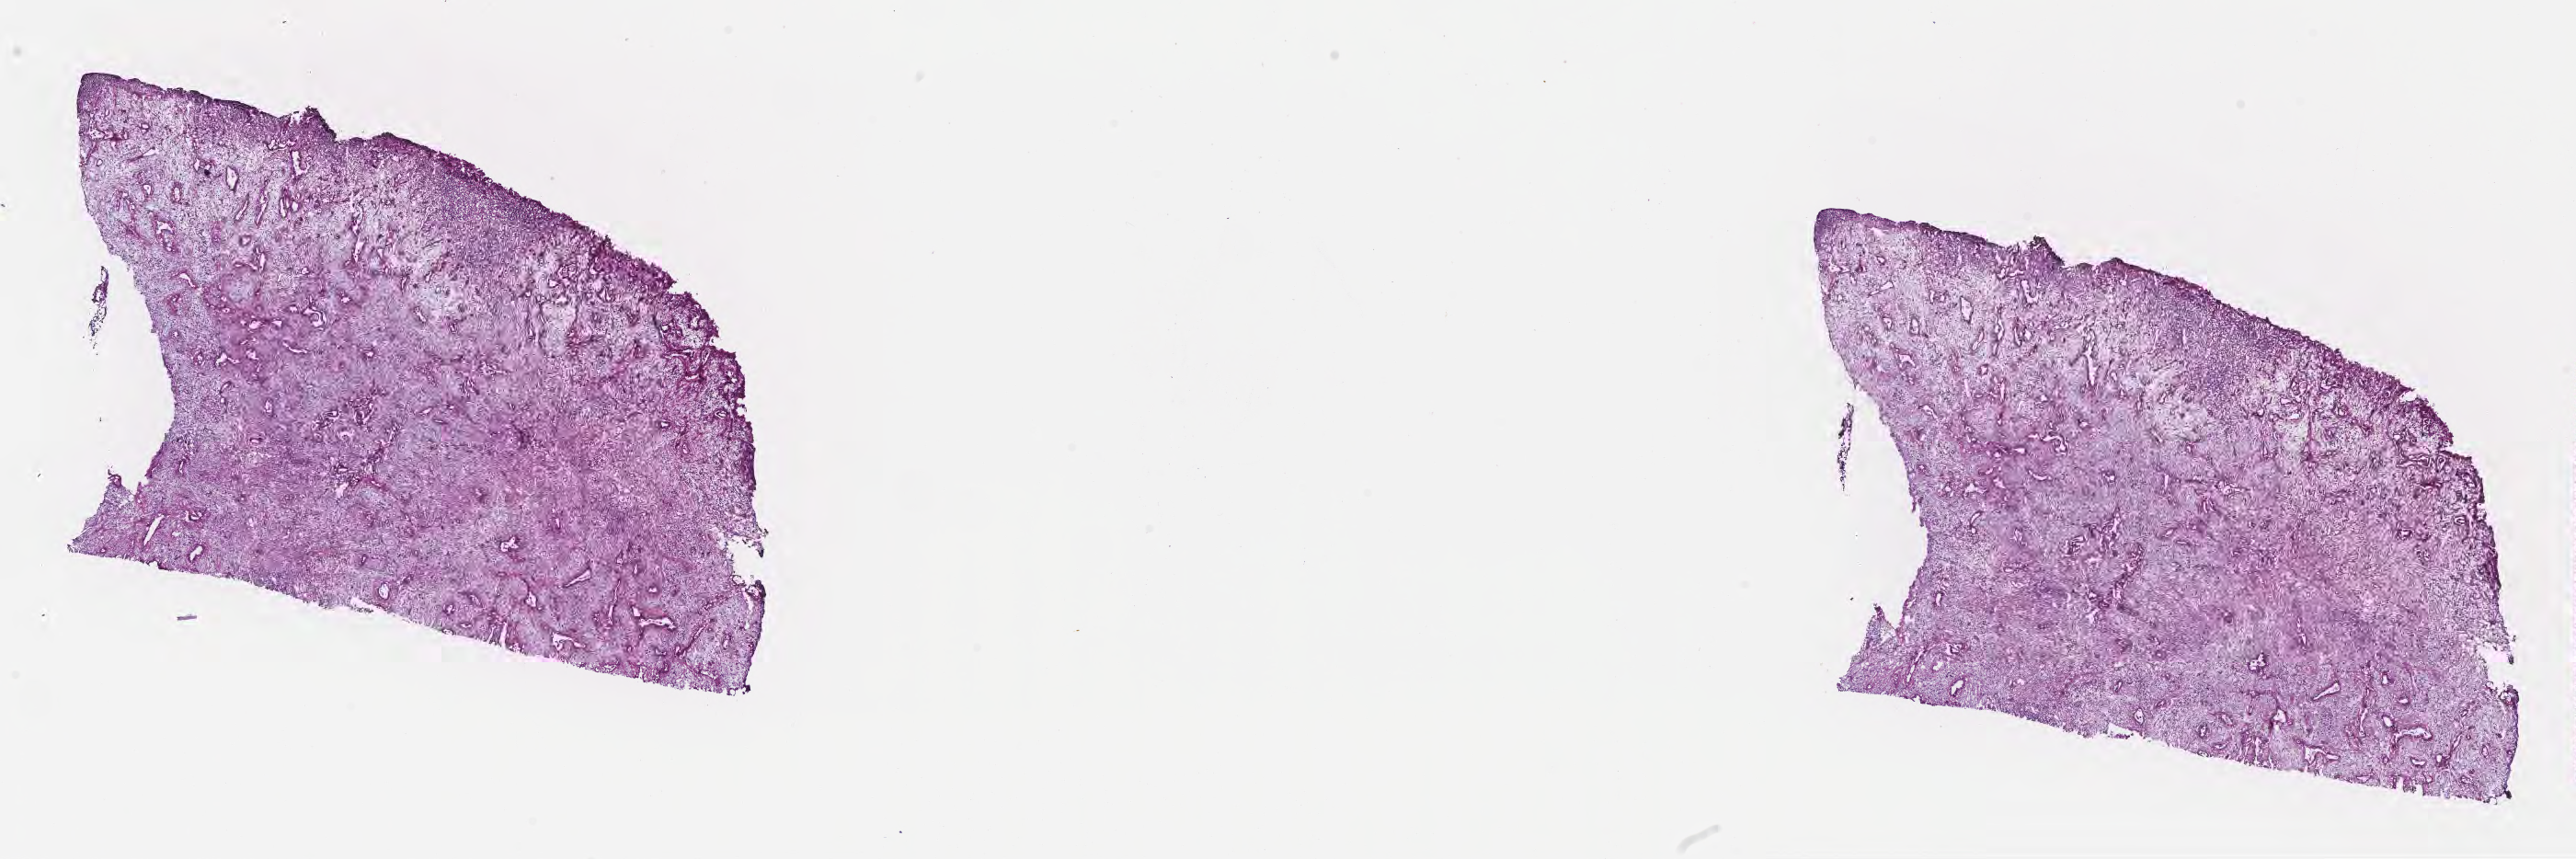
Digitized hematoxylin and eosin (H&E)-stained section, whole scanned area (about 22.6 x 7.6 mm) shown as a low-resolution overview, cryosection, specimen: metastatic tumor tissue, resected from lymph node. Patient: male, age at initial diagnosis 61 years. Composition of this section per pathologist review: tumor cells 45%, tumor nuclei 45%, stromal cells 35%, necrosis 0%, normal cells 20%. Inflammatory infiltration, as recorded: lymphocyte infiltration 8%, monocyte infiltration 9%, neutrophil infiltration 9%.
Patient diagnosis (primary): Adenocarcinoma, NOS.